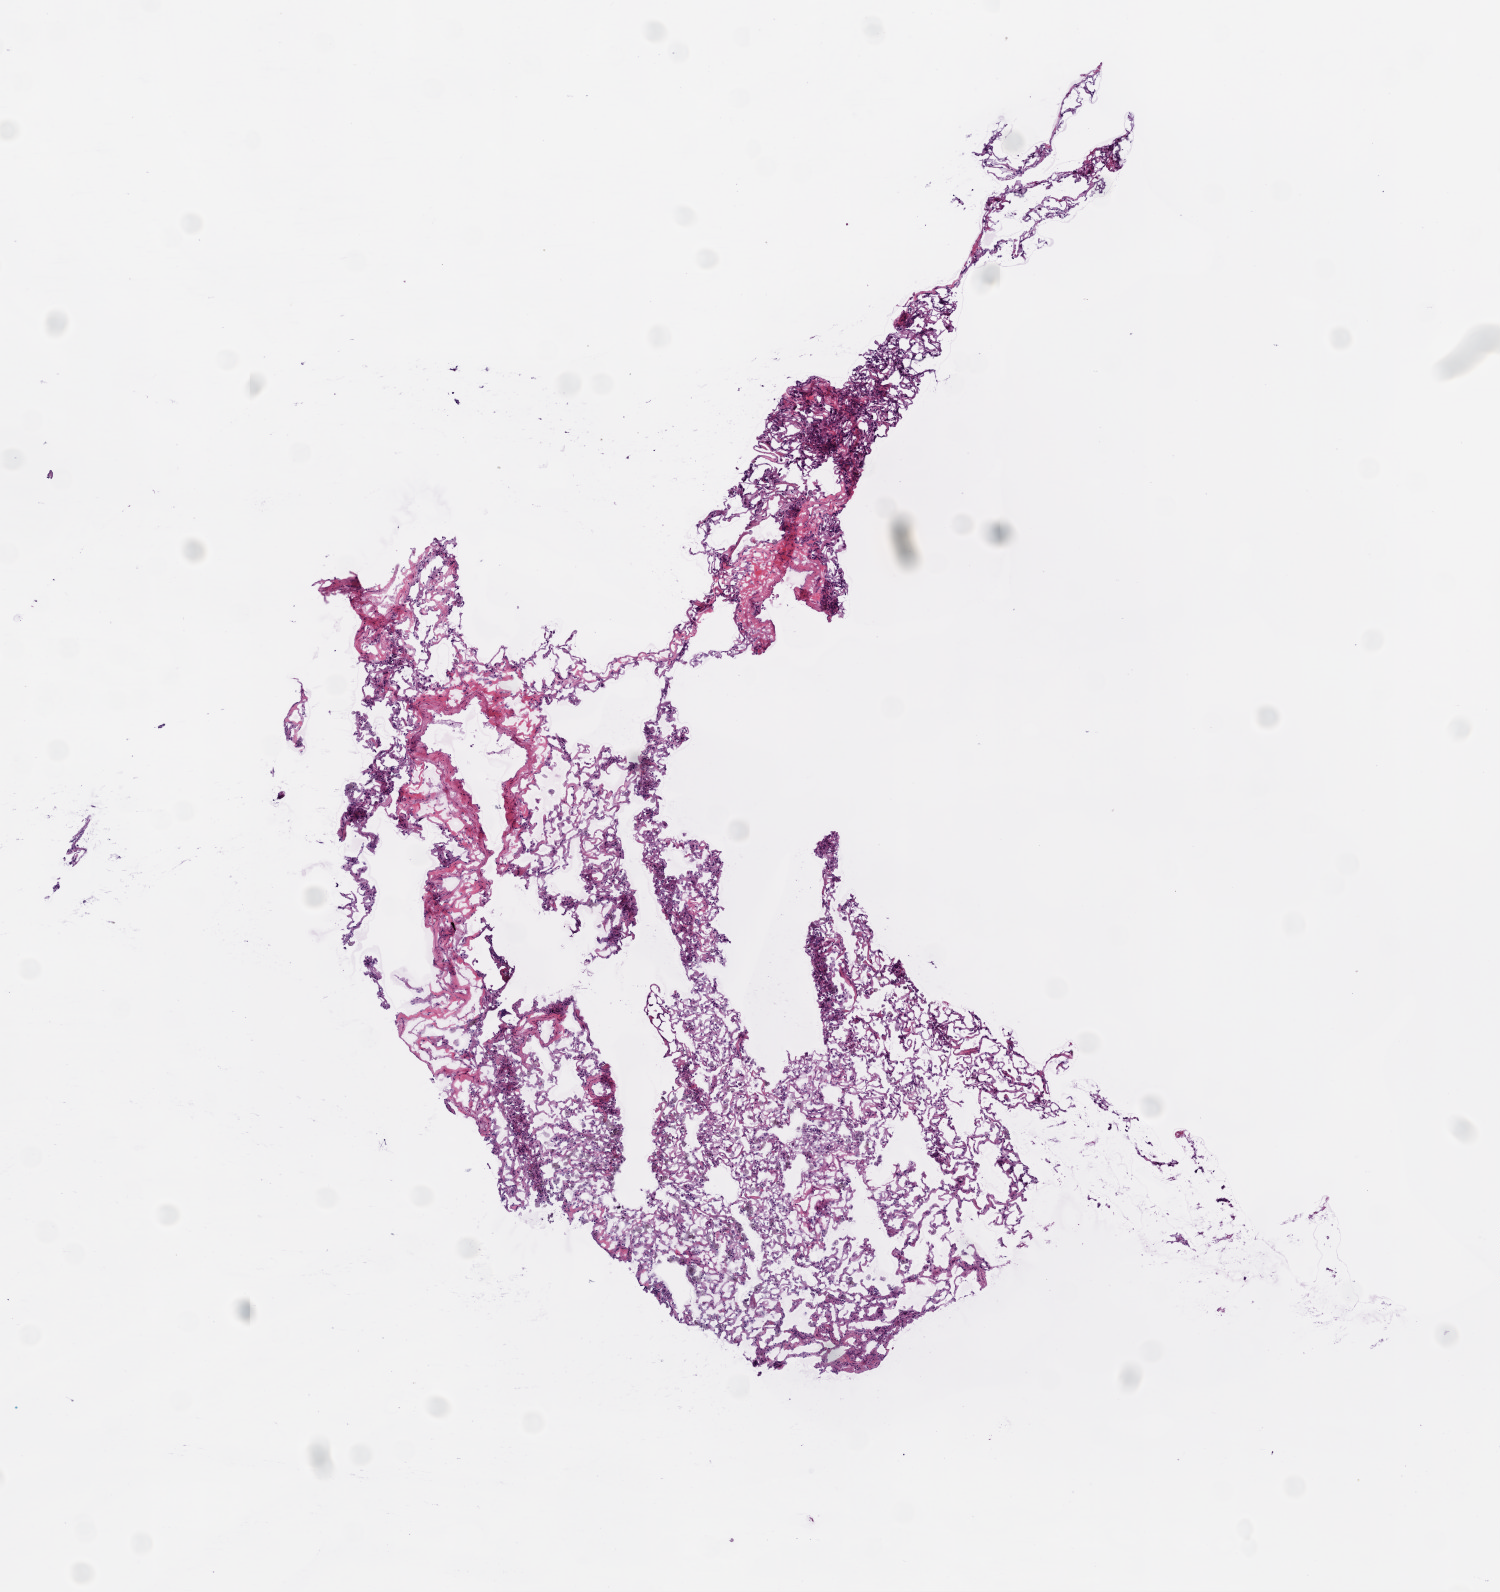
Digitized H&E tissue section (whole slide), a low-resolution overview of the entire scanned area, about 6.0 x 6.4 mm (acquisition: 20x scan); frozen section from the bottom of the tissue portion; lung, solid tissue normal (non-tumour tissue) sample. Male, age 65 years at initial diagnosis.
This section: solid tissue normal (non-tumour) sample from the same patient. Patient diagnosis: Squamous cell carcinoma, NOS (lower lobe, lung).